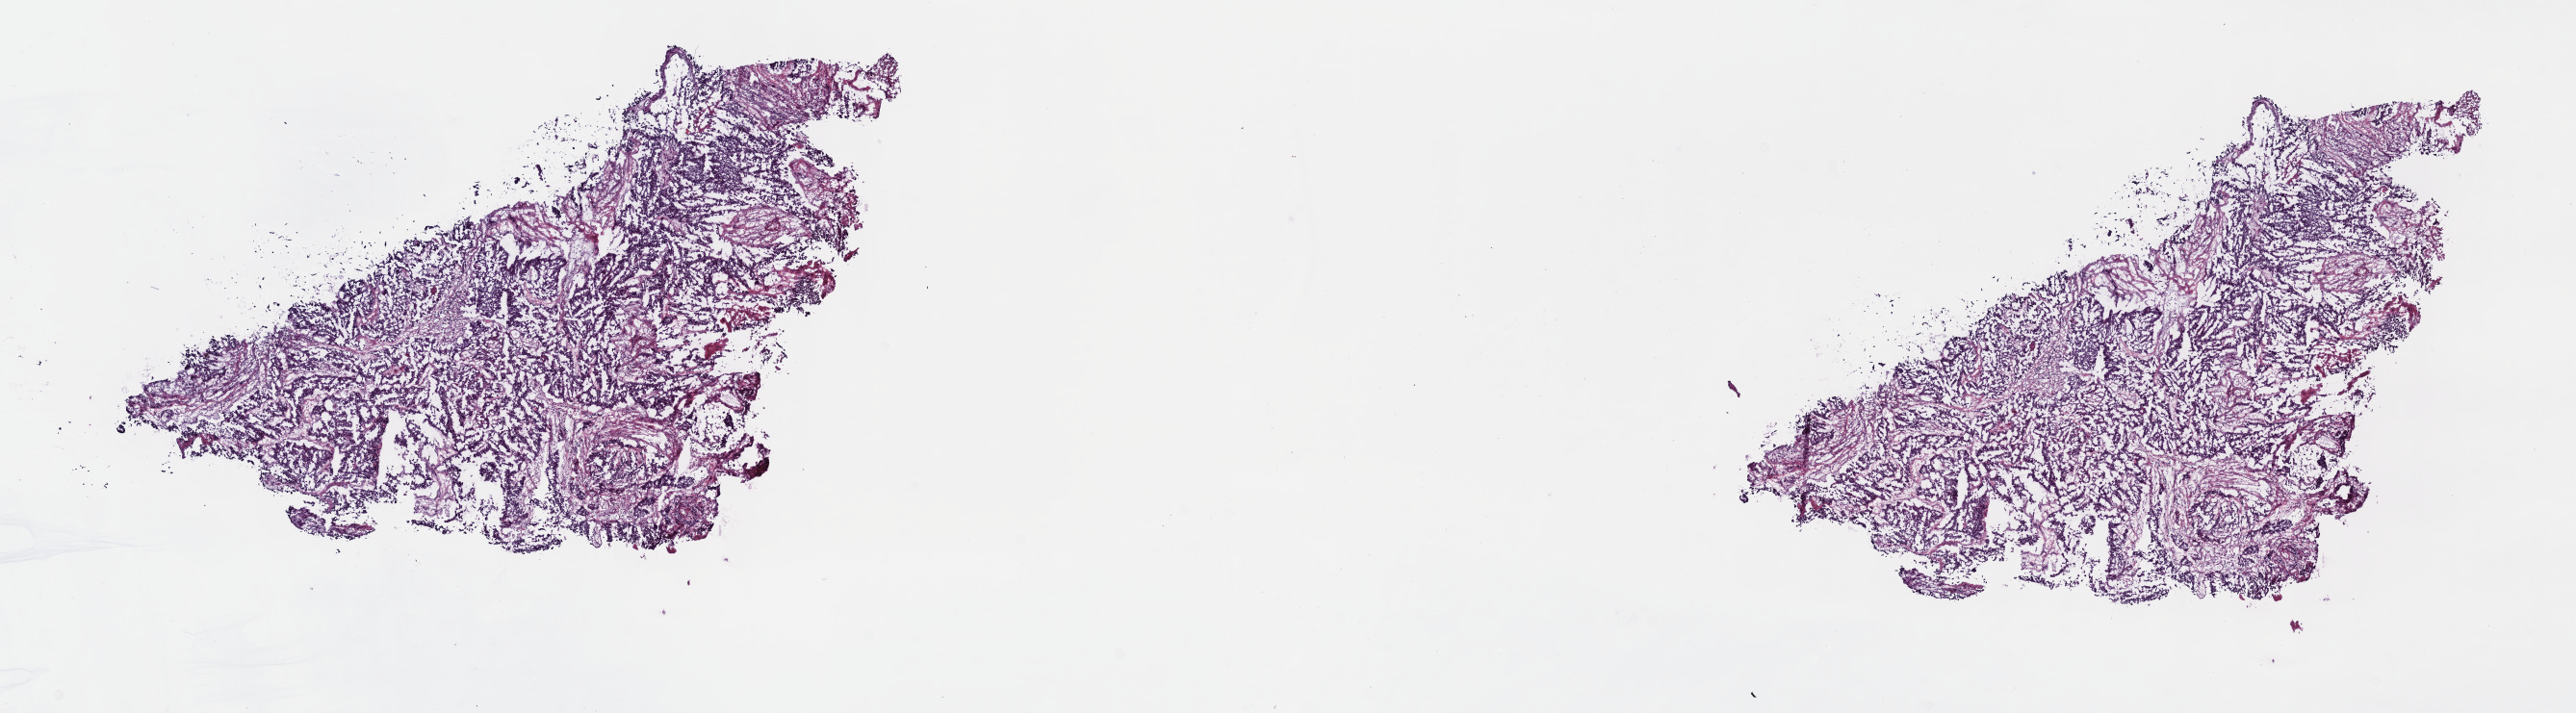
H&E whole-slide image, whole scanned area (about 21.6 x 6.0 mm, slide scanned at 40x) shown as a low-resolution overview. Frozen section. Bladder, primary tumour sample. Patient: female, age at initial diagnosis 59 years. Histologic grade: high grade. Composition of this section per pathologist review: tumour cells 100%, tumour nuclei 70%, normal cells 0%, stromal cells 0%, necrosis 0%. Infiltration values recorded for this section: lymphocyte infiltration 3%, monocyte infiltration 0%, neutrophil infiltration 0%.
AJCC pathologic stage: III (5th edition). Lymph nodes positive (case pathology): 0 of 4 examined. Histologic diagnosis: Papillary transitional cell carcinoma.